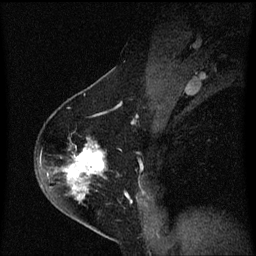
Breast MRI (dynamic contrast-enhanced), one sagittal slice; position 40 of 60 along the scan axis; dynamic contrast-enhanced series, image 2 of 3 at this slice position (ordered by acquisition); 1.5 T; TE 4.2 ms, TR 8.4 ms; 256 × 256 image matrix, field of view 200 × 200 mm. Patient: female, 54 years. From the clinical record (not read from this slice): setting: breast cancer imaged before/during neoadjuvant chemotherapy; receptor status: HER2-positive.
Structures marked on this image (semi-automatically segmented with operator editing):
- analysis volume of interest (the breast-tissue region the enhancement analysis was run in; not a lesion): bounding box <36,140,109,213> (left, top, right, bottom; pixels)
- tumour enhancement mask (voxels above the 70 % enhancement threshold inside the analysis volume of interest): <62,144,105,199>